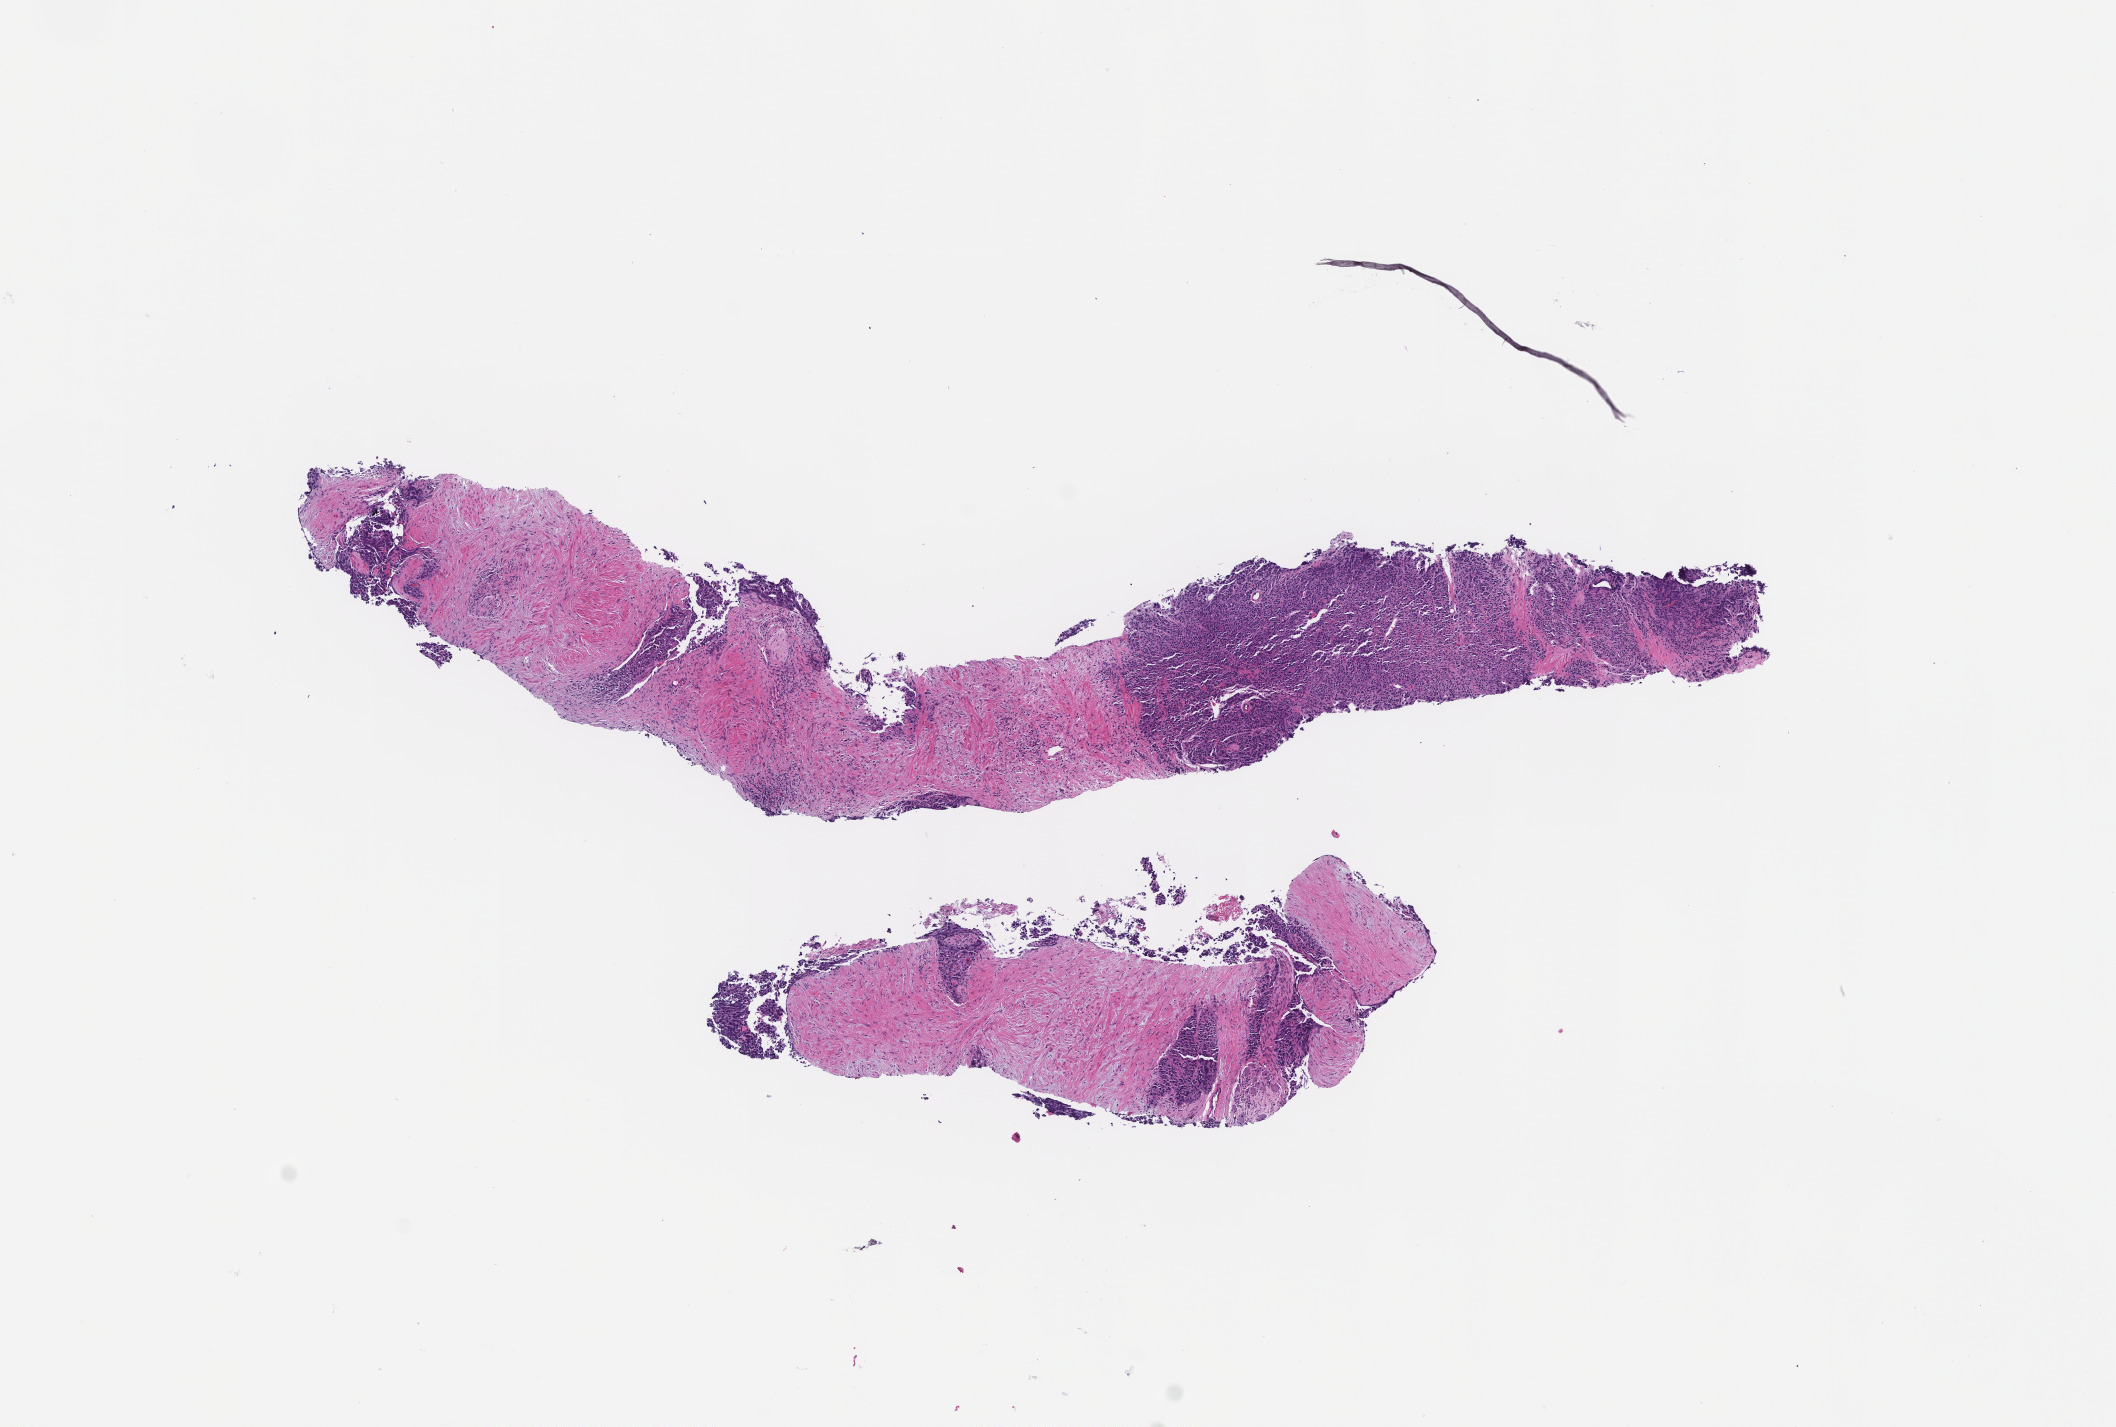
Digitized H&E-stained section — low-resolution overview of the scanned area, about 8.5 x 5.8 mm; formalin-fixed paraffin-embedded section; tissue site: prostate. Patient sex: male.
This section: primary tumour tissue. Diagnosis: Prostate Carcinoma.